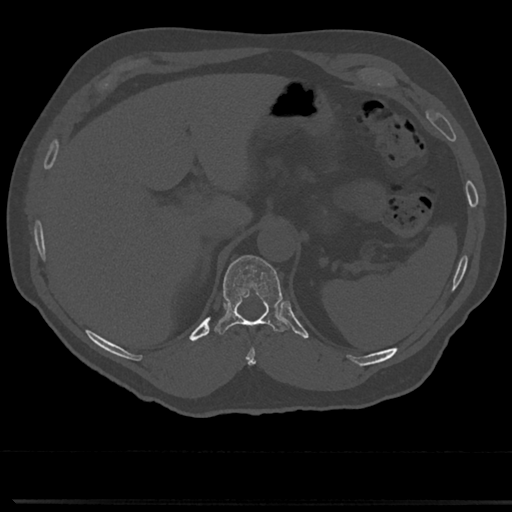
CT including the spine, one axial slice. Slice 210 of 817 in the series (ordered by position). Reconstruction kernel Br40s/3. 120 kVp. Bone window (W 1800 / L 400 HU). 0.5 mm slice thickness. 512 × 512 image matrix. Male patient, age 61 years. From the clinical record (not read from this slice): primary cancer: prostate.
Outlined on this slice (semi-automatically segmented with operator editing):
- T10 vertebra: box from (x=246, y=336) to (x=256, y=366) px
- T11 vertebra: (x=214, y=256)–(x=289, y=336)